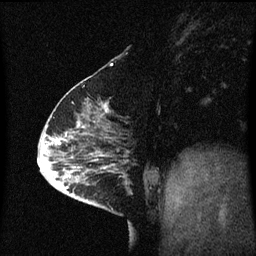
Breast MRI (dynamic contrast-enhanced), one sagittal slice. Position 20 of 60 along the scan axis. Dynamic contrast-enhanced series, image 2 of 3 at this slice position (ordered by acquisition). 1.5 T. TE 4.2 ms, TR 8.4 ms. 2 mm slice thickness. 256 × 256 image matrix, field of view 200 × 200 mm. Patient: female, 63 years.
Structures marked on this image (semi-automatically segmented with operator editing):
- analysis volume of interest (the breast-tissue region the enhancement analysis was run in; not a lesion): bounding box (x1, y1, x2, y2) in pixels: (98, 168, 131, 217)
- tumour enhancement mask (voxels above the 70 % enhancement threshold inside the analysis volume of interest): (100, 168, 105, 169)